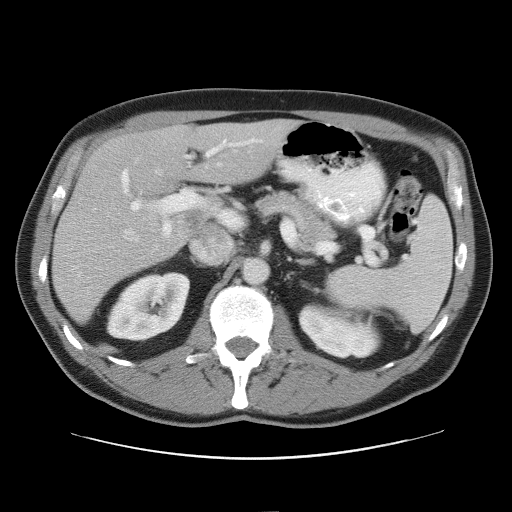
Contrast-enhanced abdominal CT, one axial slice; slice 34 of 52 in the series (ordered by position); reconstruction kernel STANDARD; soft-tissue window (W 400 / L 40 HU); 512 × 512 image matrix, field of view 393 × 393 mm. Male patient, age 70 years. From the clinical record (not read from this slice): diagnosis: colorectal cancer liver metastases, imaged before liver resection; multiple liver metastases: yes; largest metastasis: 4 cm.
Outlined on this slice (expert manual segmentation):
- hepatic veins: bounding box [x1, y1, x2, y2] px = [74, 169, 161, 268]
- liver: [54, 121, 296, 323]
- planned liver remnant (the part of the liver to remain after resection): [109, 121, 296, 187]
- portal vein (with intrahepatic branches): [121, 136, 263, 238]
- liver metastasis: [188, 214, 203, 228]